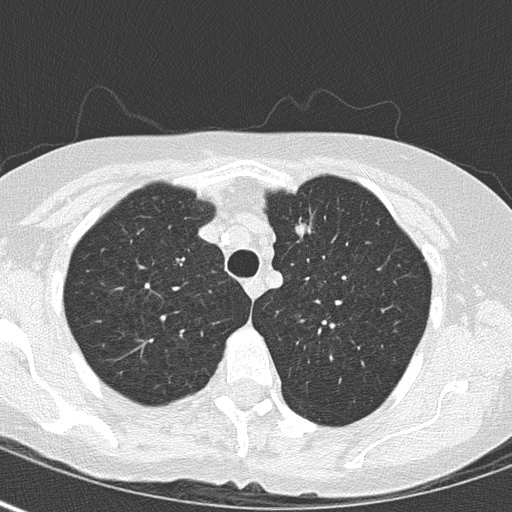
Axial slice from a low-dose chest CT screening exam. Second annual screen. Lung window (W 1500 / L -600 HU). 2 mm slice thickness. Slice 40 of 163 in the series. 512 × 512 image matrix, field of view 280 × 280 mm. Female participant, aged 64 years at enrolment.
Expert reader's lesion annotation, bounding box (x1, y1, x2, y2) in pixels: (277, 211, 321, 258). The exam's reader record, not a measurement of the box and not confirmed to be the same lesion: non-calcified nodule or mass ≥4 mm, left upper lobe, 8 × 7 mm, pre-existing on the prior screen: yes. Official screen result: positive, other.